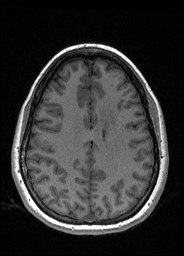
Pre-operative brain MRI before brain-tumour surgery, one axial slice; slice 69 of 176 in the series (ordered by position); T1-weighted post-contrast; 1 mm slice thickness; 184 × 256 image matrix, field of view 180 × 250 mm. From the clinical record (not read from this slice): histopathology: Oligodendroglioma; WHO grade: 2; IDH mutation: yes; tumour location: Left Frontal.
Outlined on this slice (outlined manually by an expert reader):
- tumour: bounding box <100,109,116,125> (left, top, right, bottom; pixels)